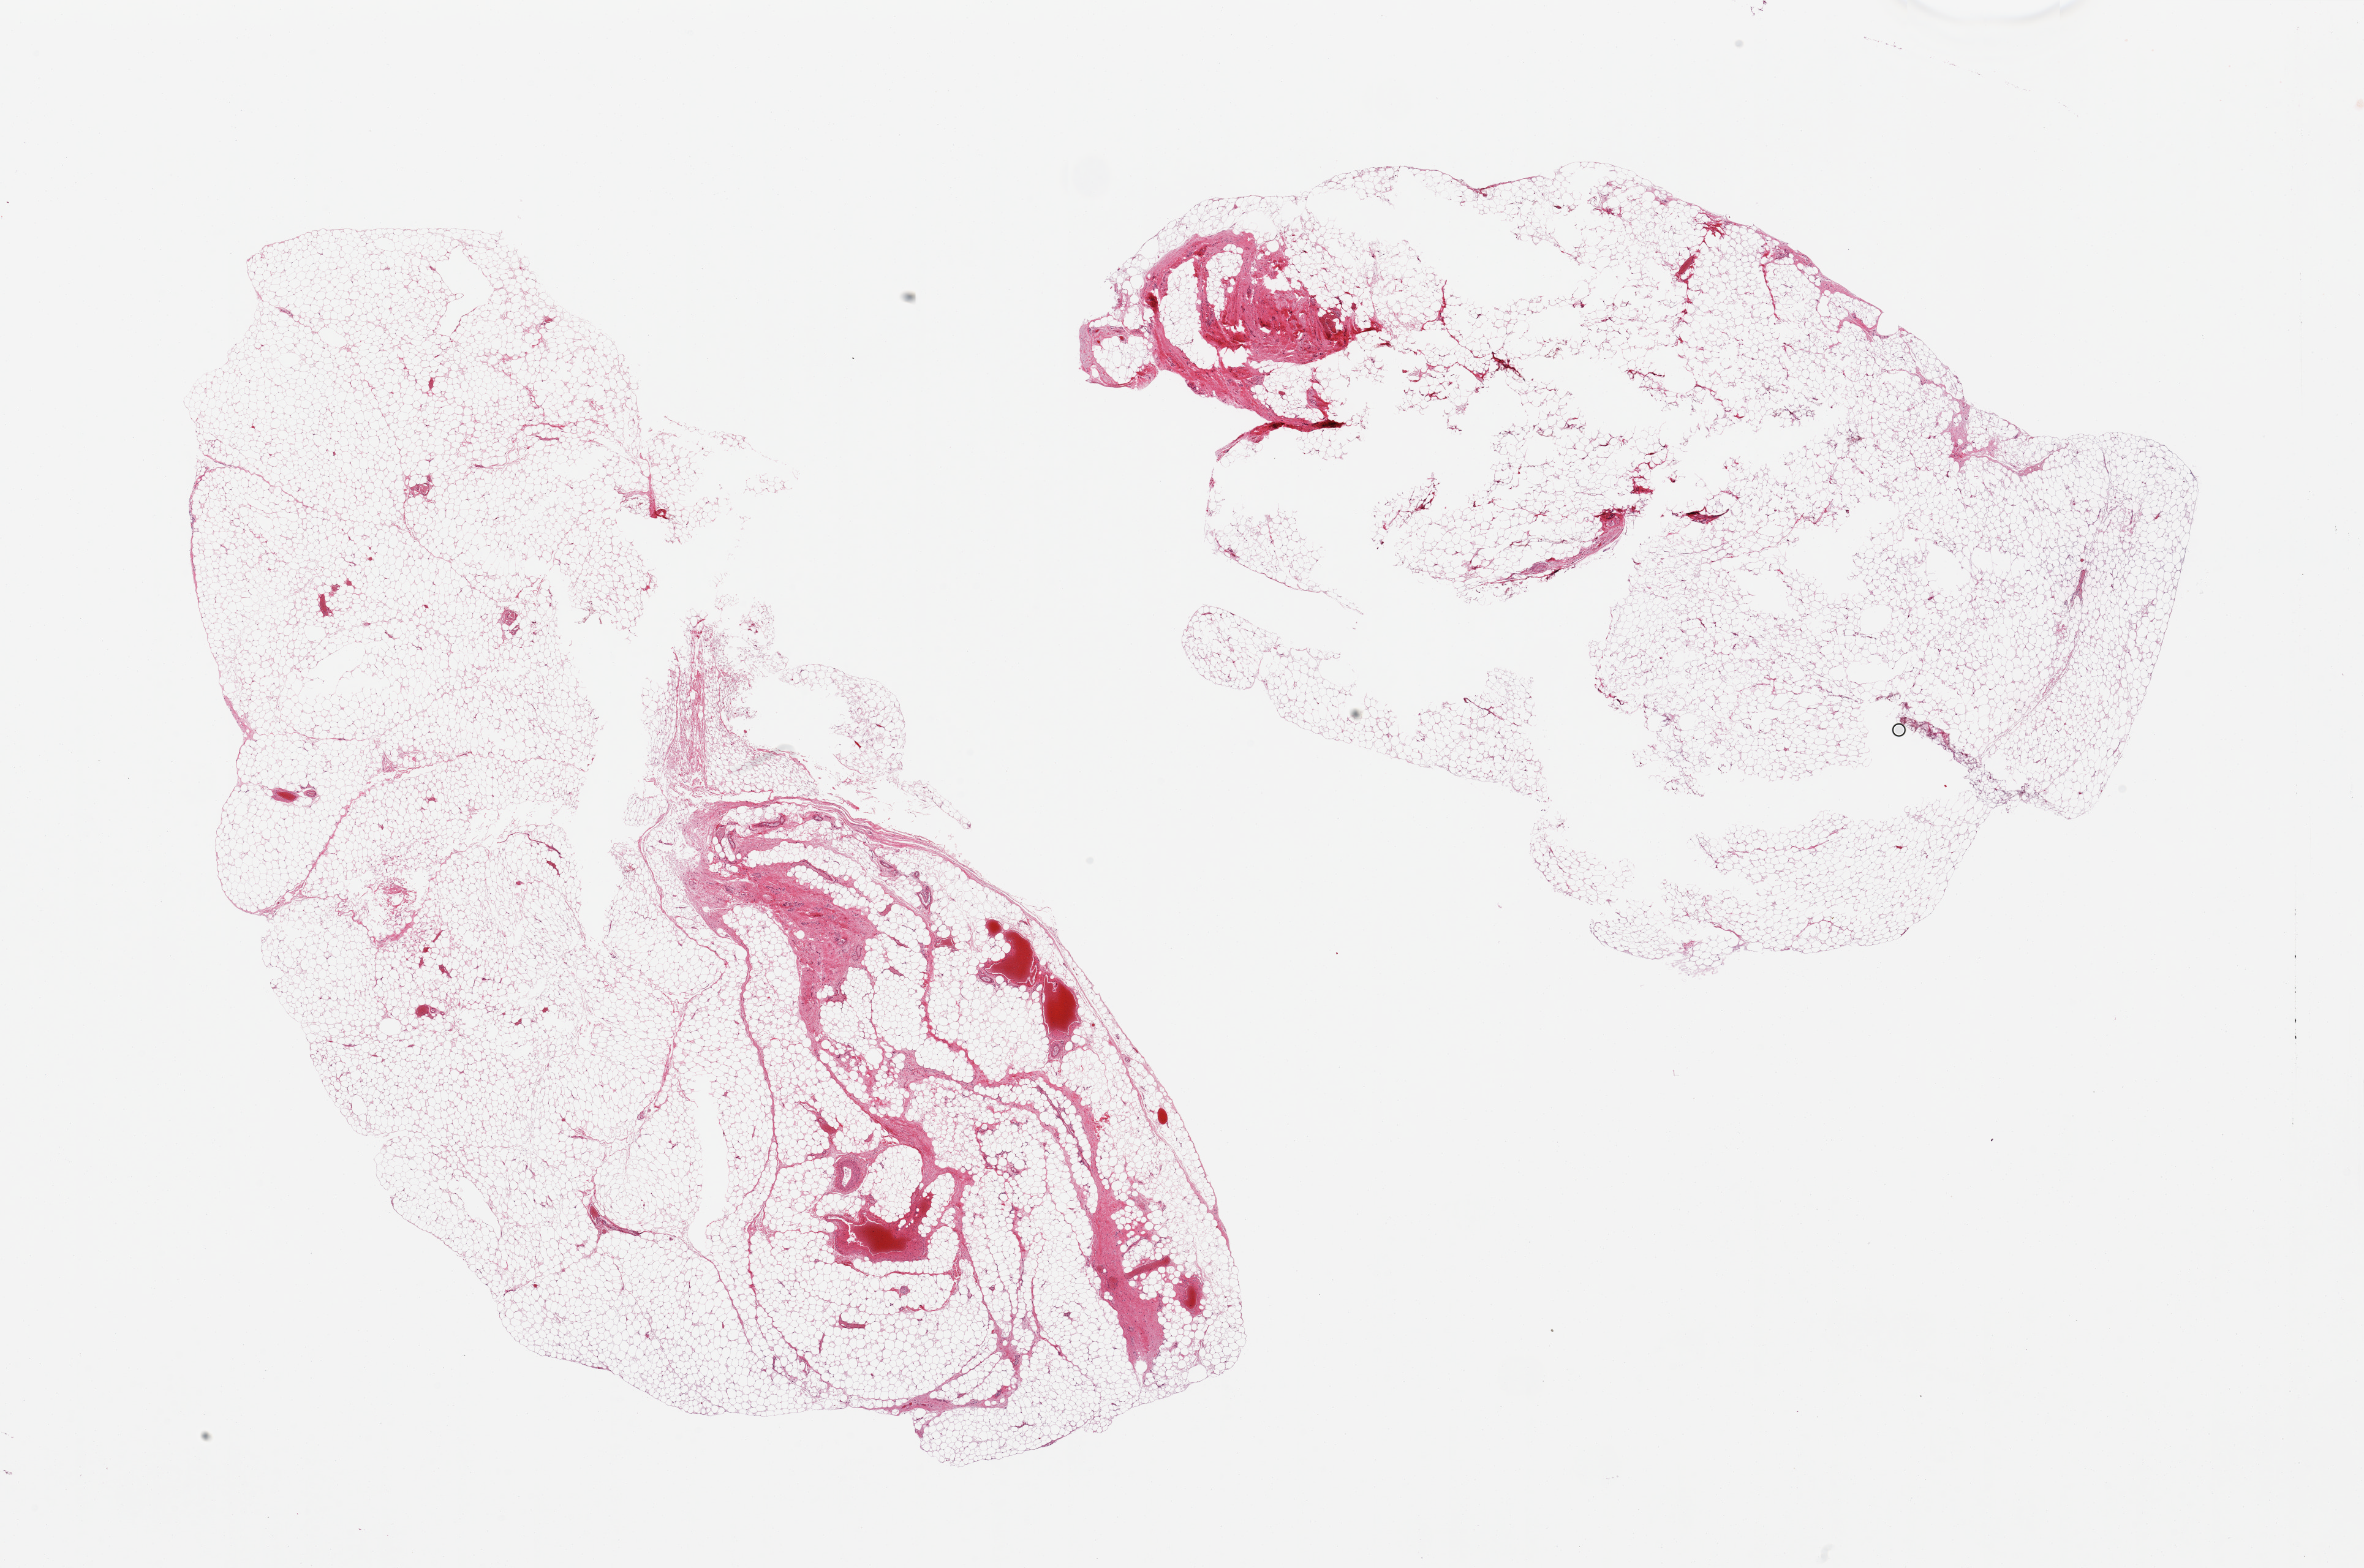
Digitized hematoxylin and eosin (H&E)-stained section — low-resolution overview of the scanned area, about 30.5 x 20.2 mm; PAXgene-fixed paraffin-embedded (PFPE) section; target tissue: omentum; tissue donor sample. Donor sex: male.
Review note (as recorded): 2 pieces ~10% facisa.